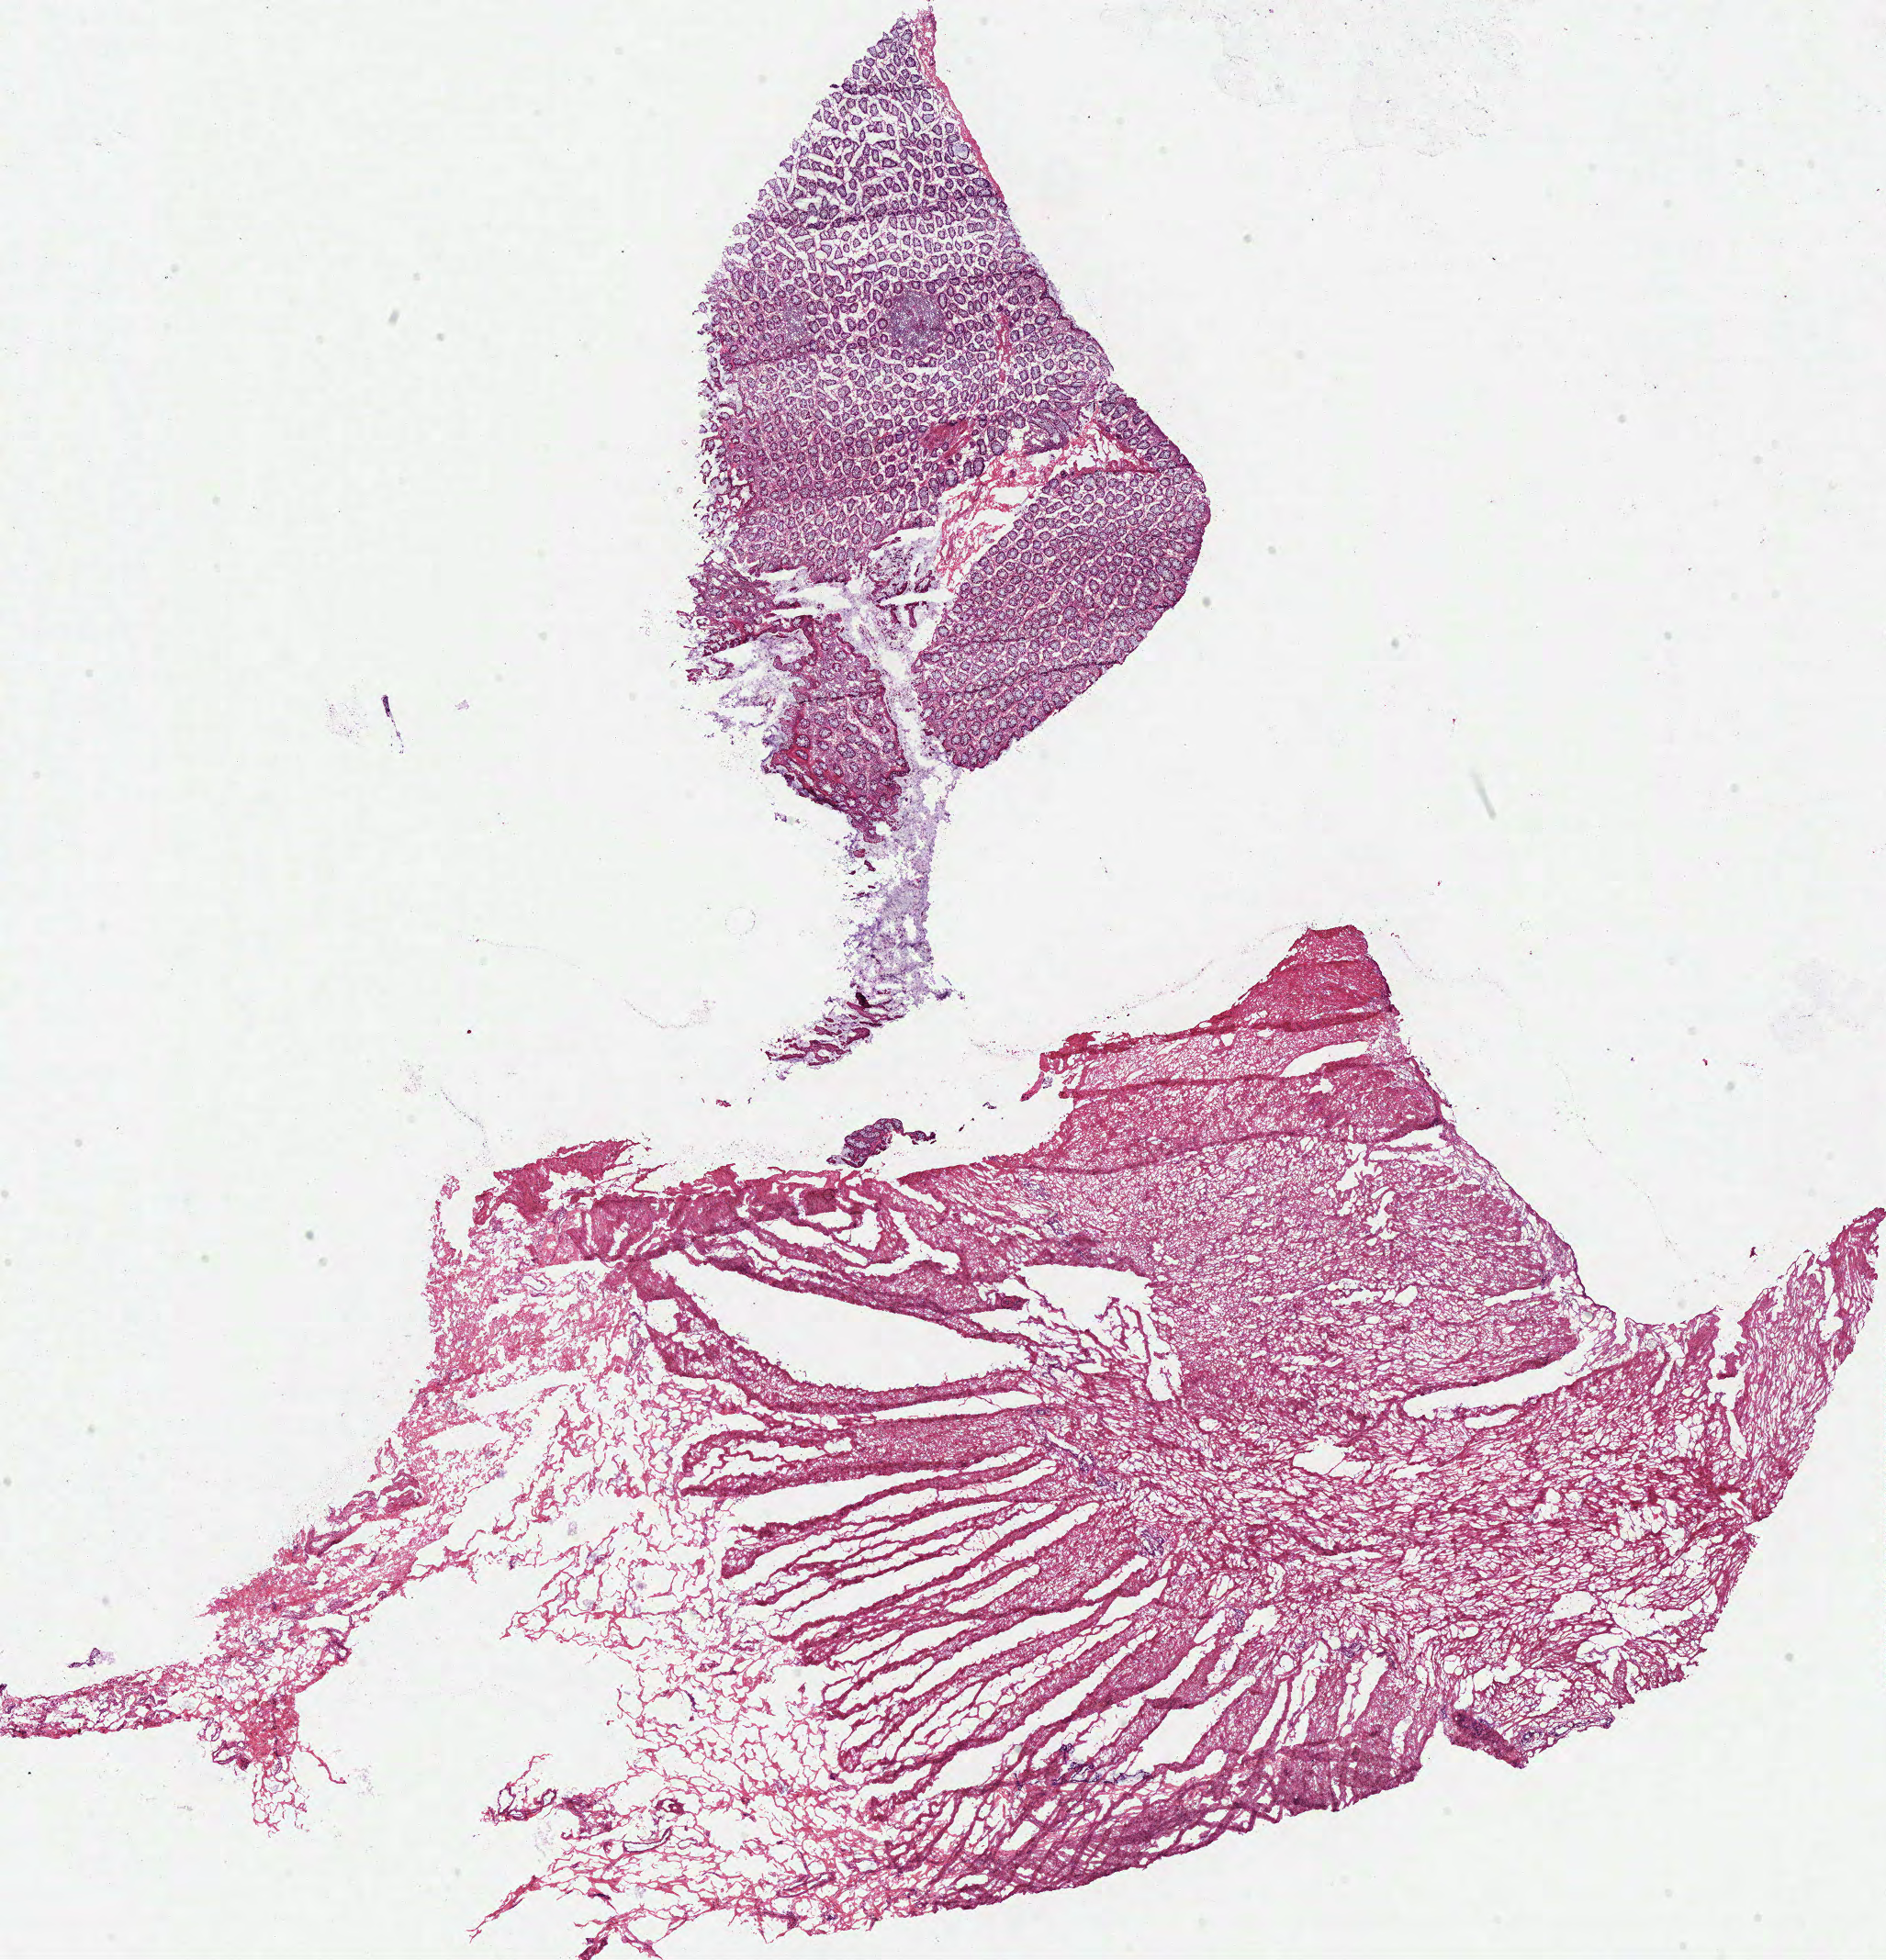
Whole-slide histology image, H&E-stained, whole scanned area (about 16.2 x 16.8 mm, slide scanned at 40x) shown as a low-resolution overview; frozen section from the top of the tissue portion; solid tissue normal (non-tumour tissue) sample from the colon. Male patient; age at initial diagnosis 69 years.
* this section: solid tissue normal (non-tumour) sample from the same patient
* patient diagnosis: Adenocarcinoma, NOS (sigmoid colon)